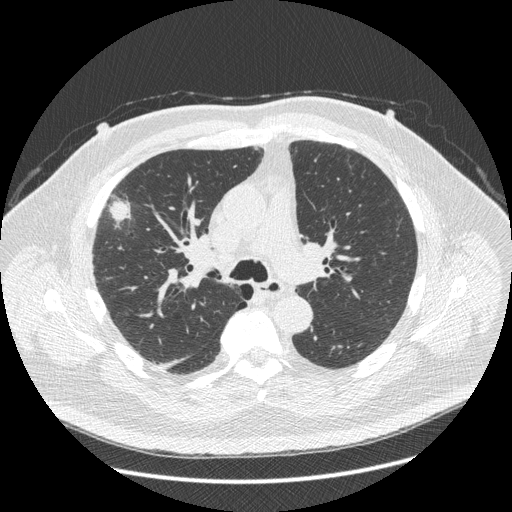
Low-dose screening chest CT, one axial slice. Position 273 of 426 along the scan axis. Reconstruction kernel STANDARD. 120 kVp. Lung window (W 1500 / L -600 HU). 1.25 mm slice thickness. 512 × 512 image matrix, field of view 400 × 400 mm.
Annotated regions visible in this slice (manually delineated by an expert):
- lesion 1 (tumor, upper lobe of right lung): bounding box [x1, y1, x2, y2] px = [110, 202, 129, 221]